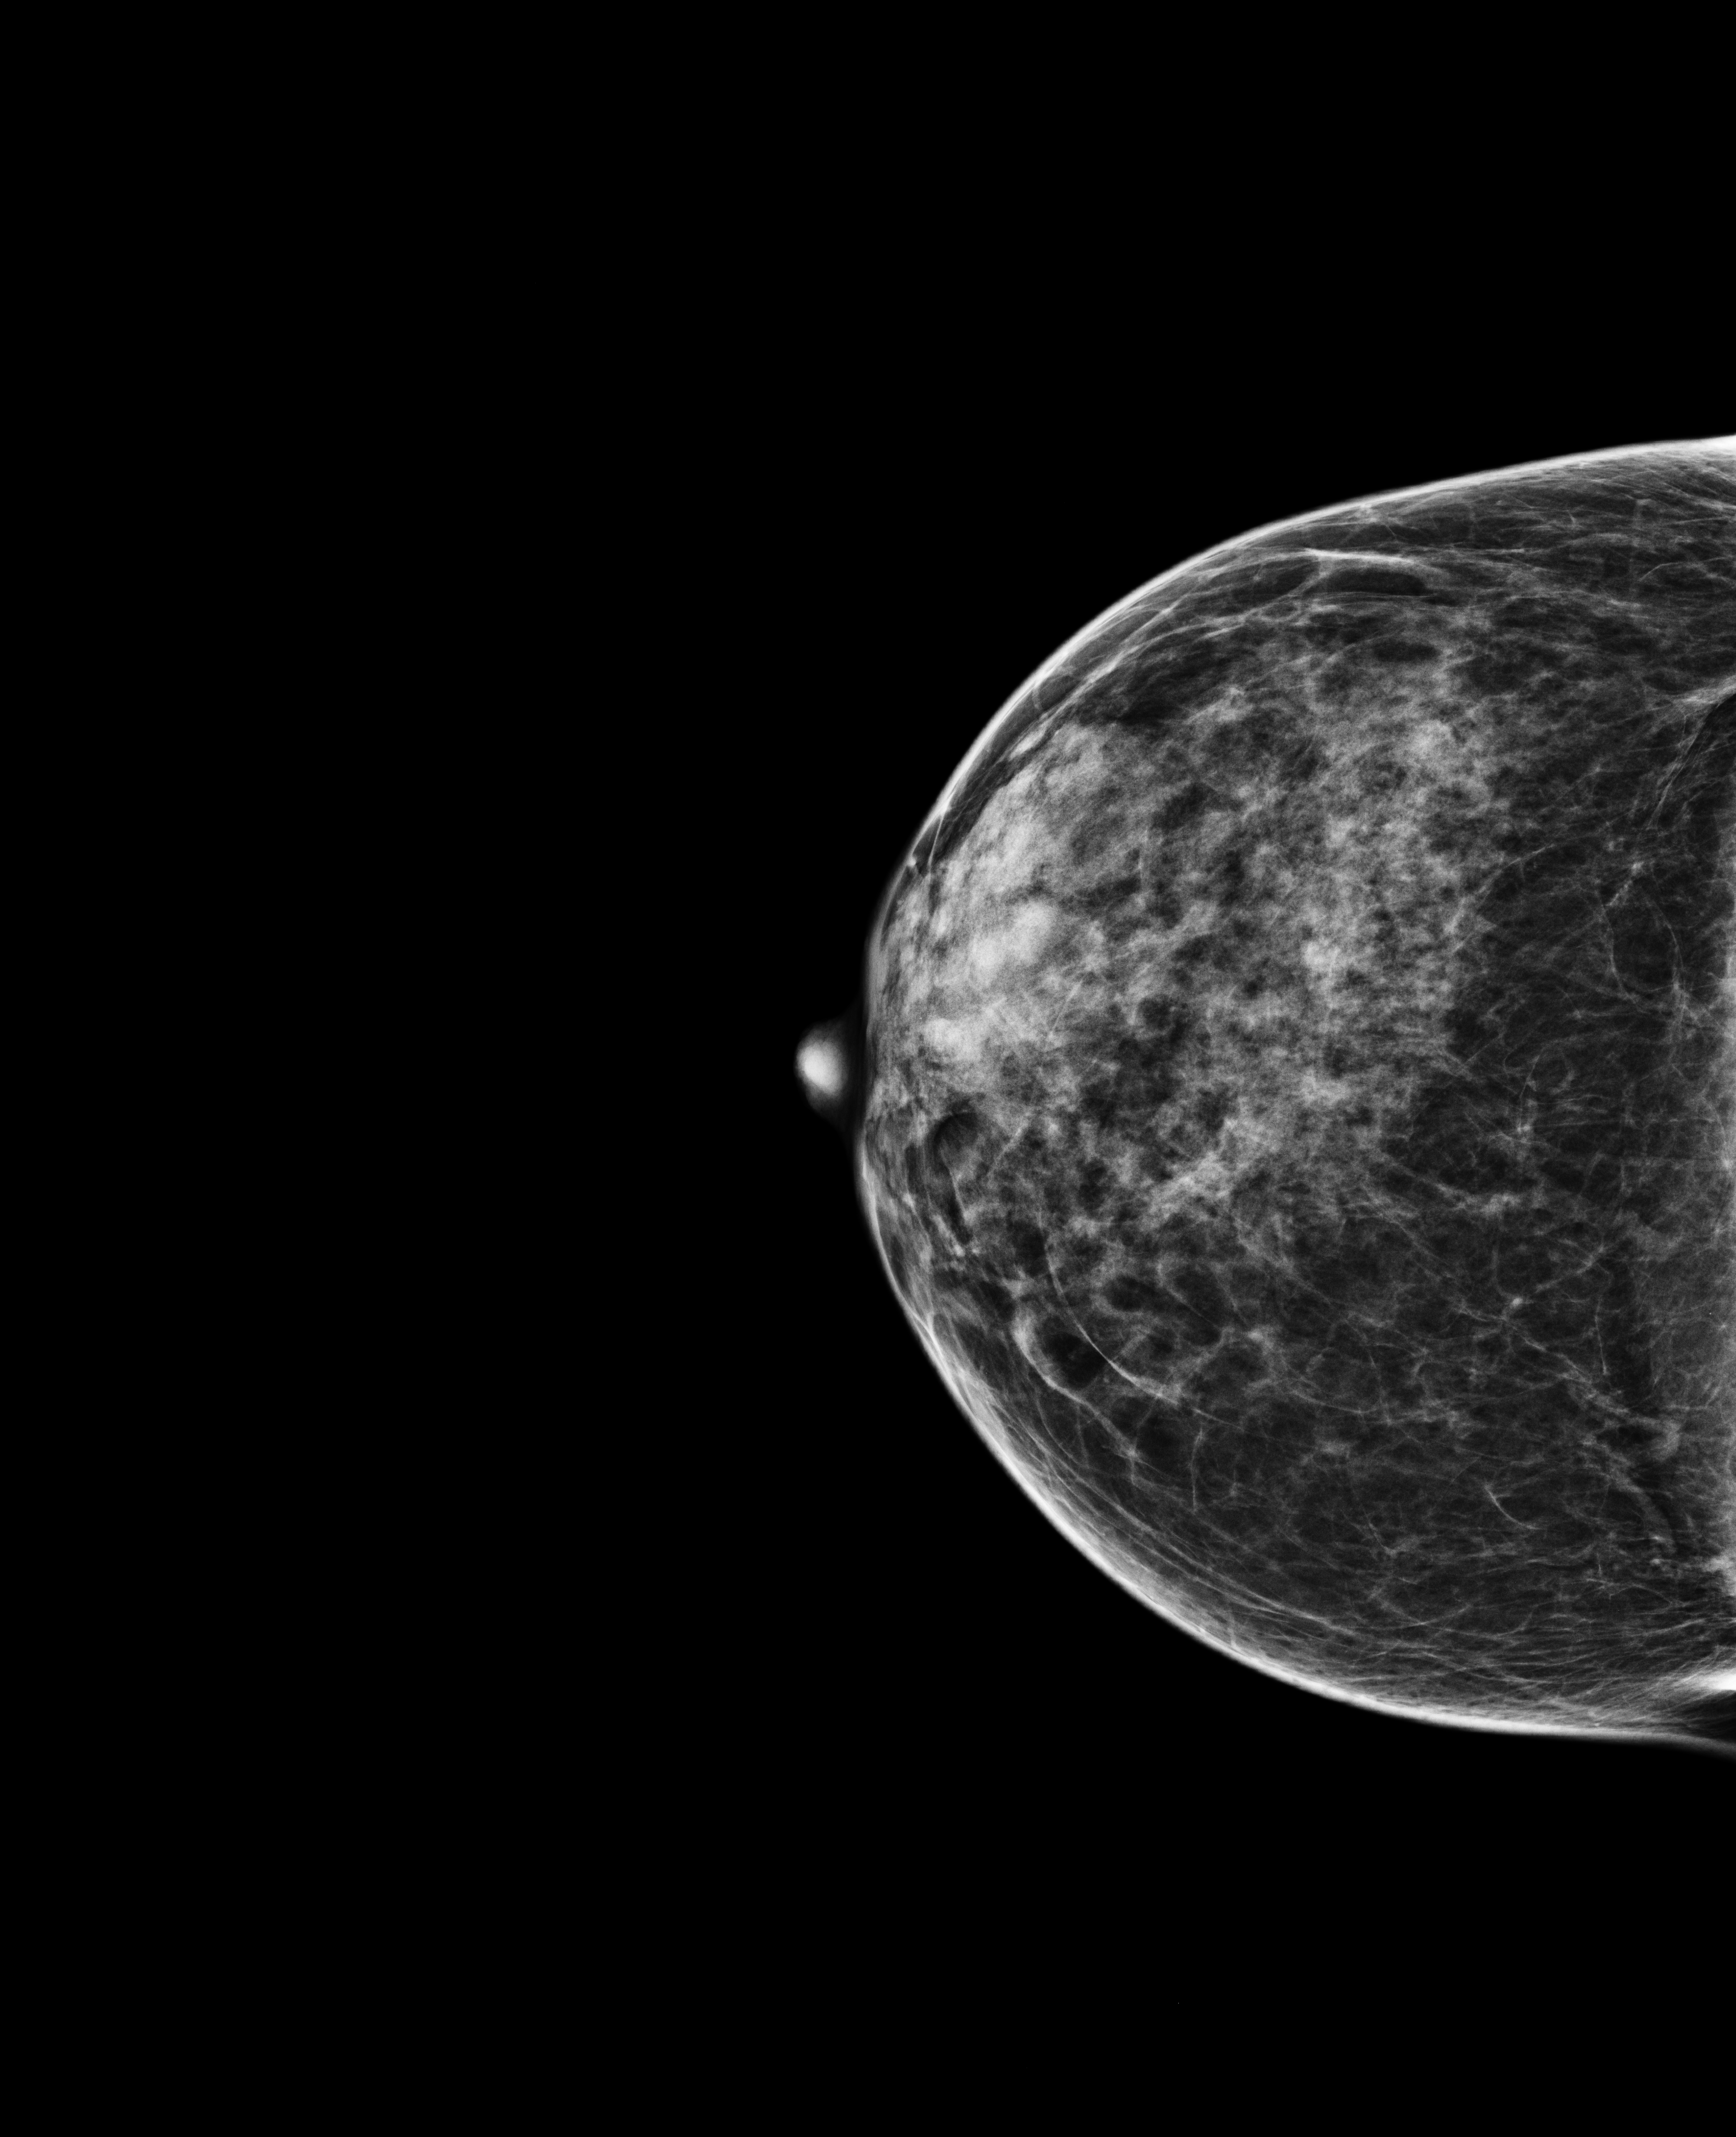
Annual screening mammography examination, system: Selenia Dimensions. Patient aged 51 years (female).
Image type: full-field digital mammogram. Breast: right. Projection: craniocaudal (CC) view.